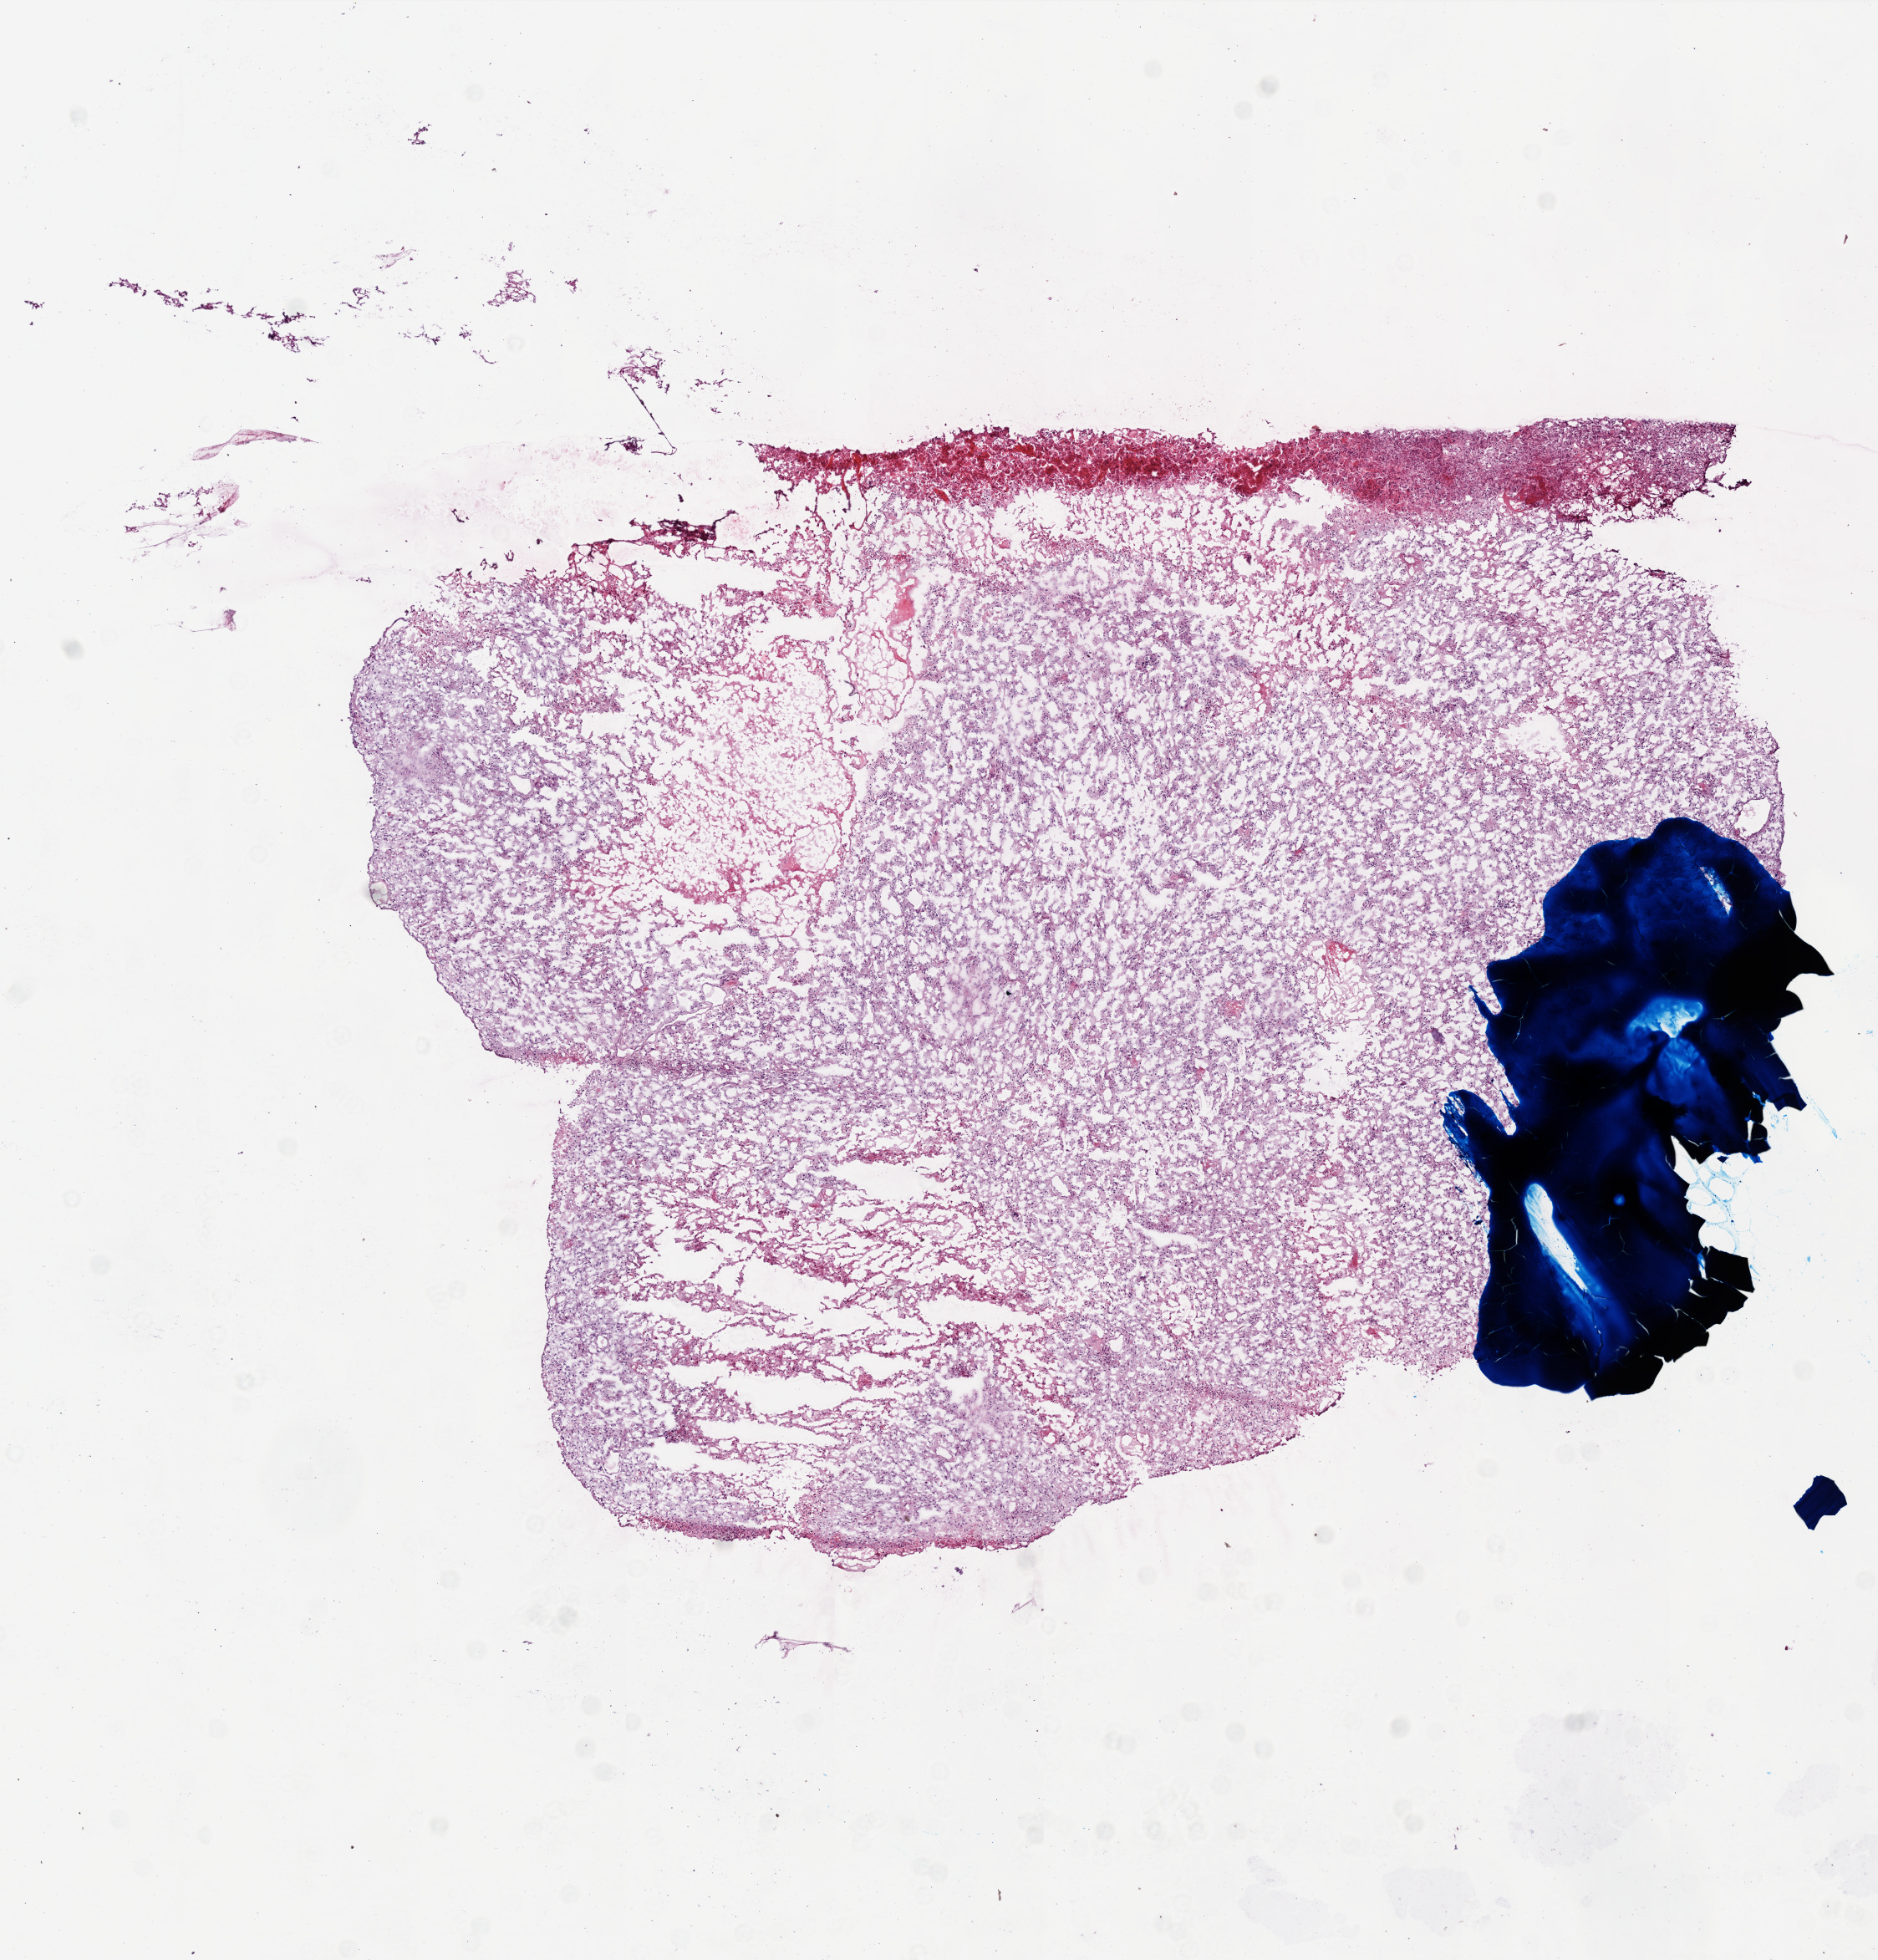
H&E whole-slide image, whole scanned area (about 9.0 x 9.4 mm, acquisition: 20x scan) shown as a low-resolution overview. Frozen section. Primary tumour sample from the brain. Patient: male, age at initial diagnosis 14 years. Pathologist review of this section (percent, as recorded): tumour cells 80%, tumour nuclei 100%, normal cells 0%, stromal cells 0%, necrosis 20%. Inflammatory infiltration, as recorded: lymphocyte infiltration 0%.
Diagnosis: Glioblastoma.